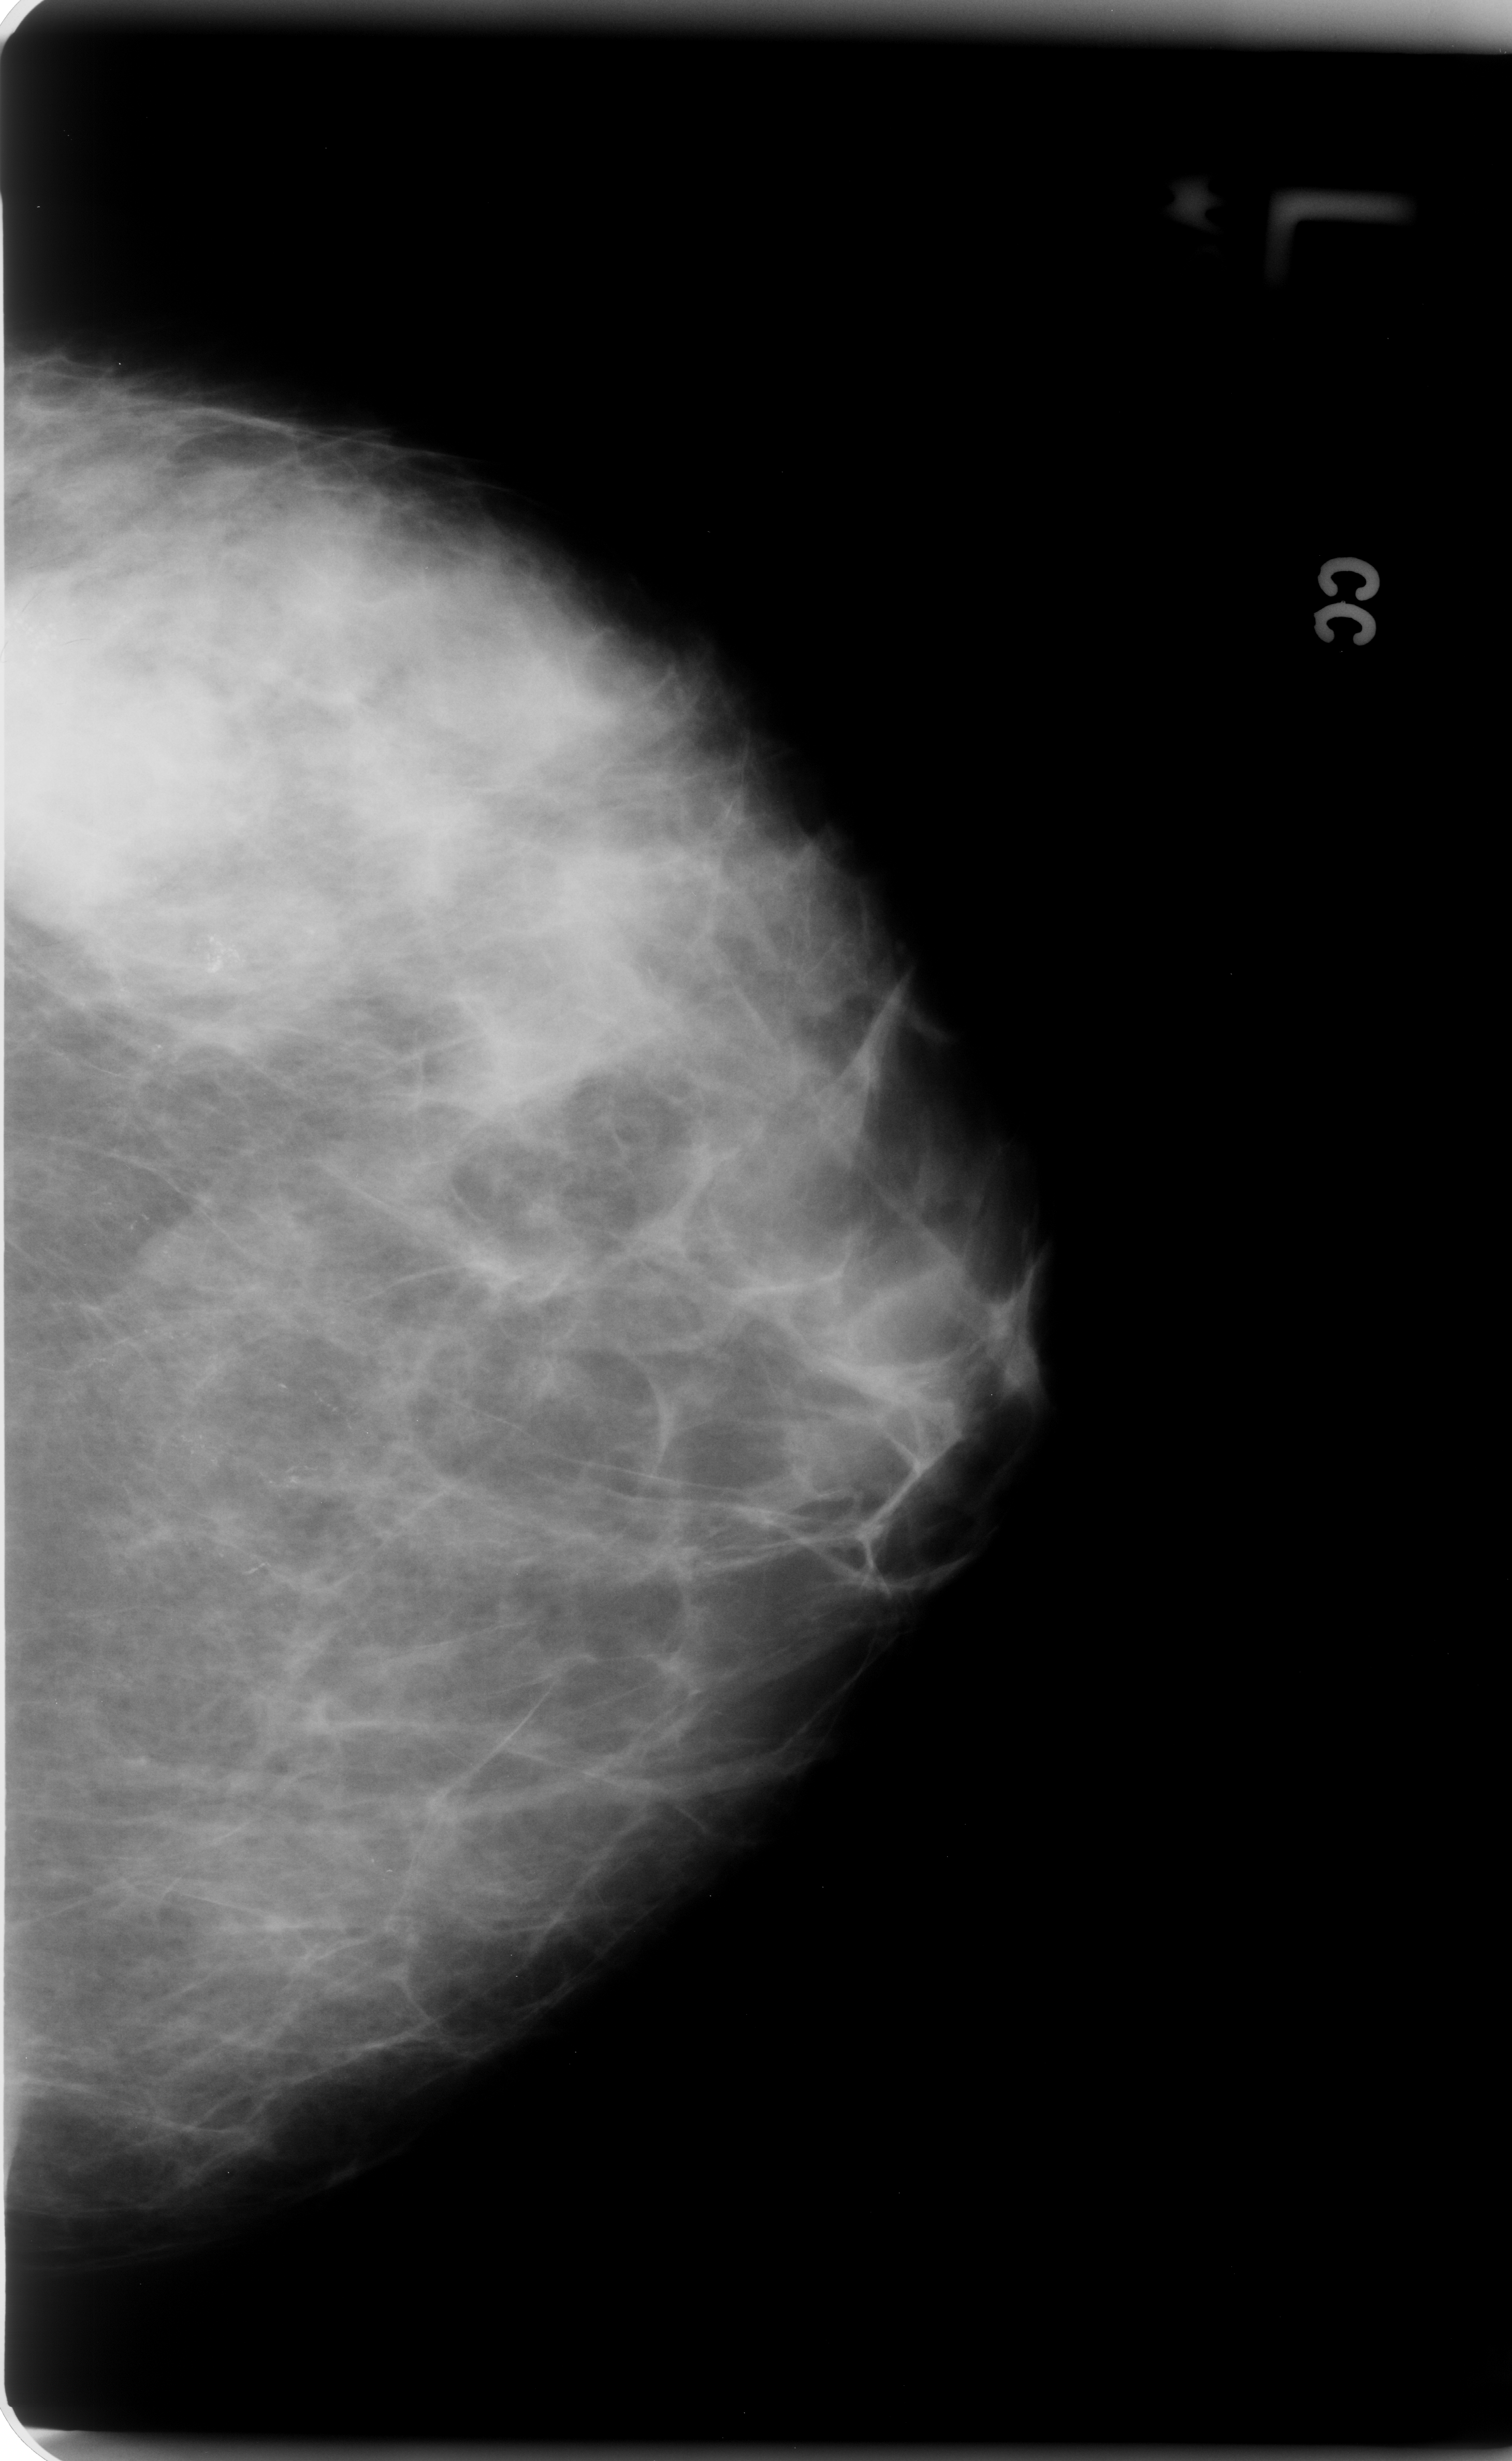
Mammogram (digitized film), left breast, CC view, breast composition: scattered fibroglandular densities (BI-RADS density category 2 of 4).
Radiologist-marked abnormalities on this image: Finding 1 of 2: calcifications, morphology pleomorphic / fine linear branching, distribution regional; BI-RADS assessment category 5; pathology (as recorded): malignant. Finding 2 of 2: calcifications, morphology pleomorphic / fine linear branching, distribution regional; BI-RADS assessment category 5; pathology (as recorded): malignant.